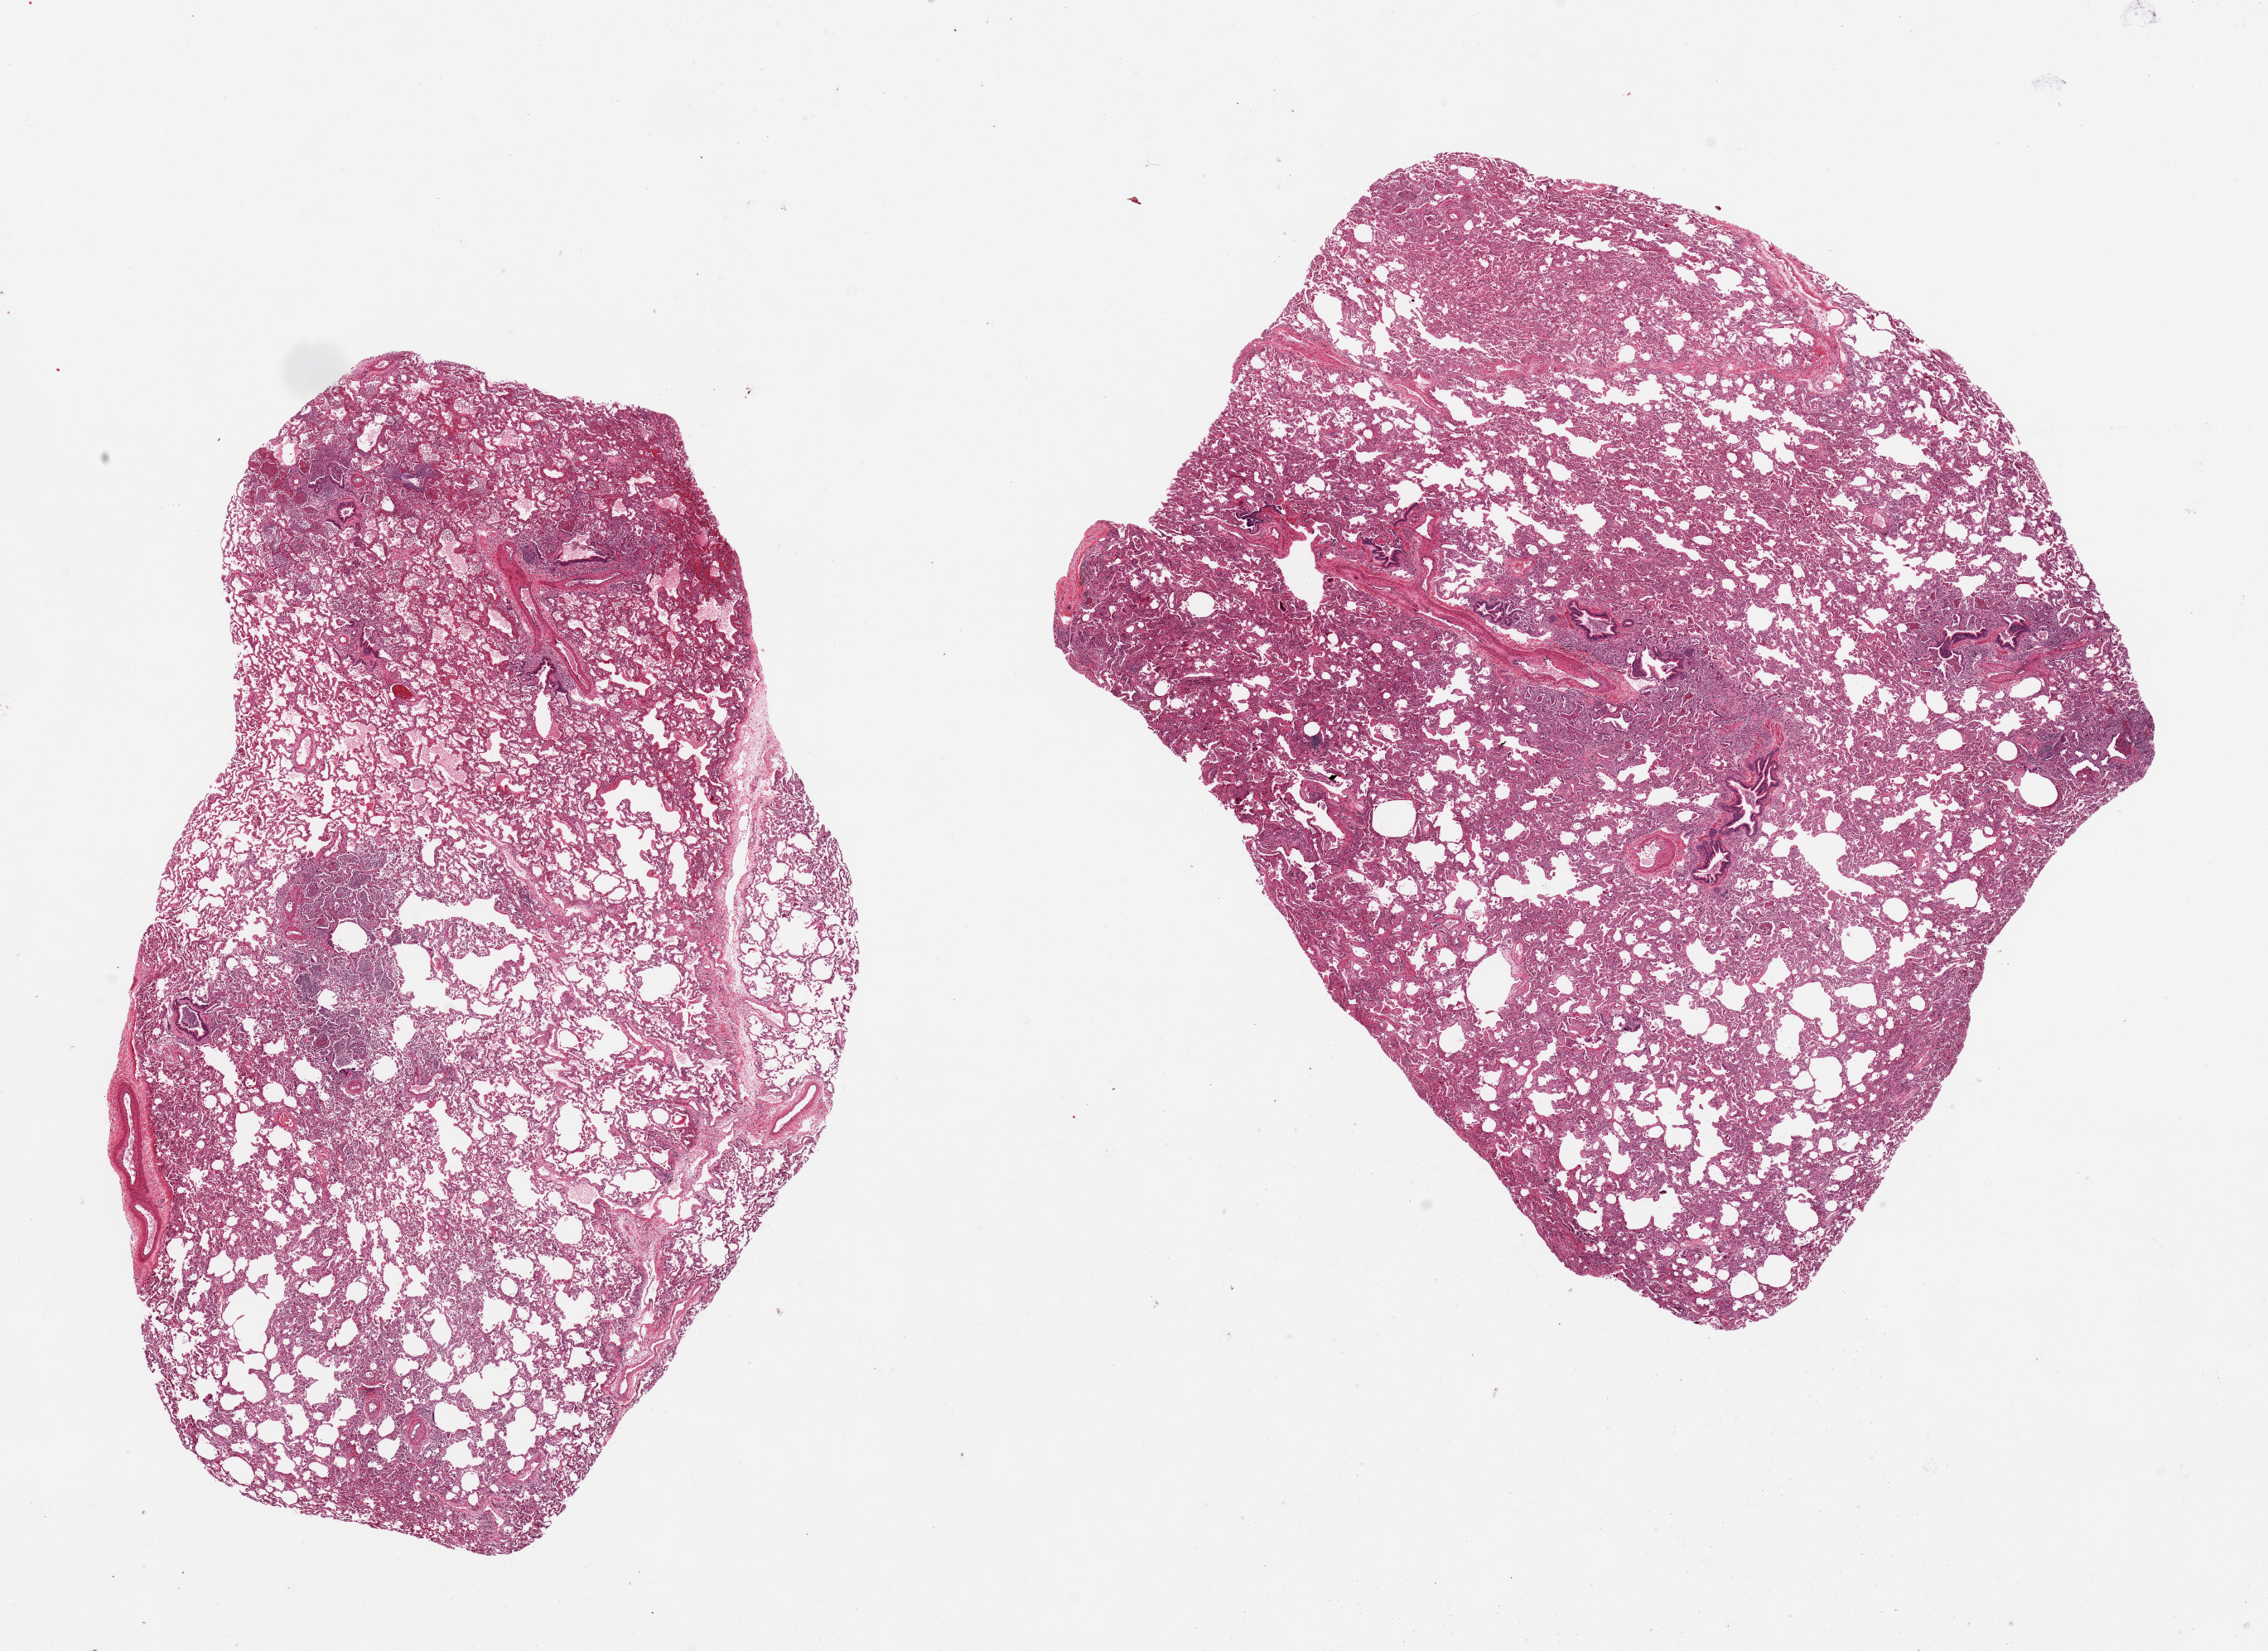
Whole-slide image, haematoxylin and eosin stain — a low-resolution overview of the entire scanned area, about 21.7 x 15.8 mm; PAXgene-fixed paraffin-embedded (PFPE) section; target tissue: lung; tissue donor sample. Donor sex: male.
• pathologist's review note for this sample: 2 pieces ~10x8mm, patchy acute pneumonia, representative fields